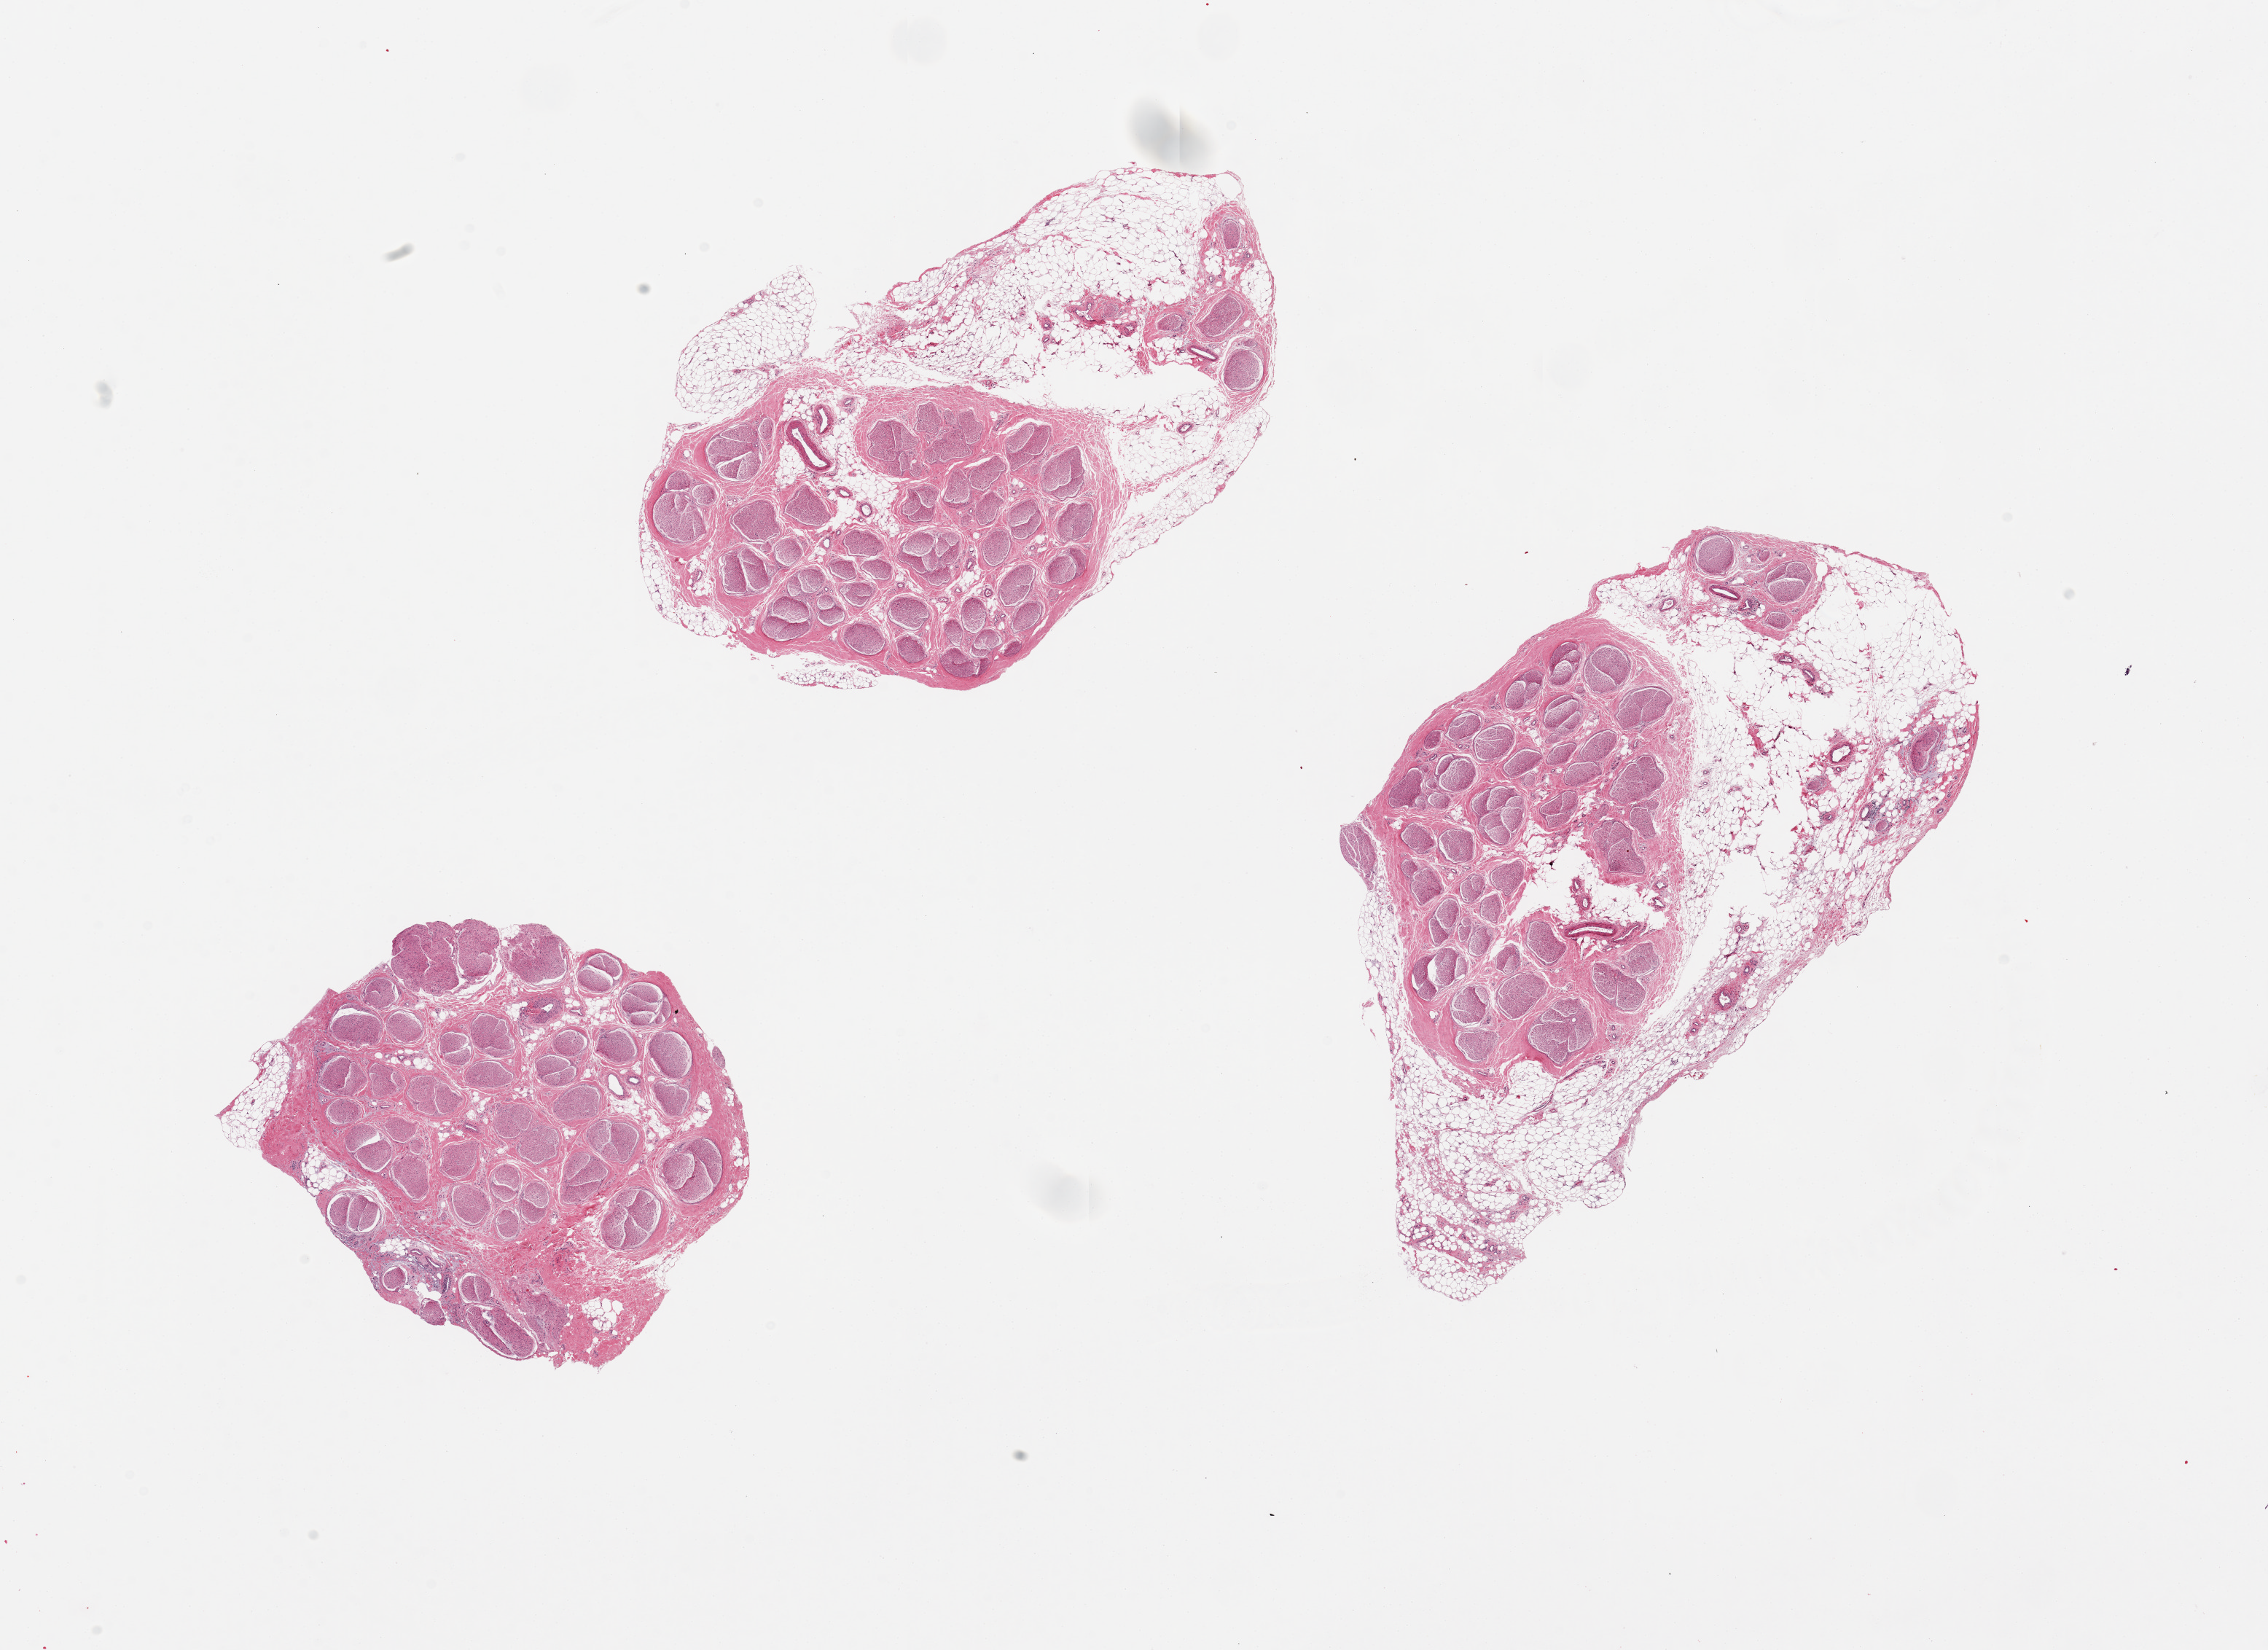
Hematoxylin and eosin (H&E) whole-slide image, brightfield, low-resolution overview of the scanned area, about 24.6 x 17.9 mm, PAXgene-fixed paraffin-embedded (PFPE) section, target tissue: tibial nerve, donor tissue sample. Female donor.
Review note (as recorded): 3 pieces ~5mm d. ; two with significant attached adipose tissue nubbins up to ~3mm thick.